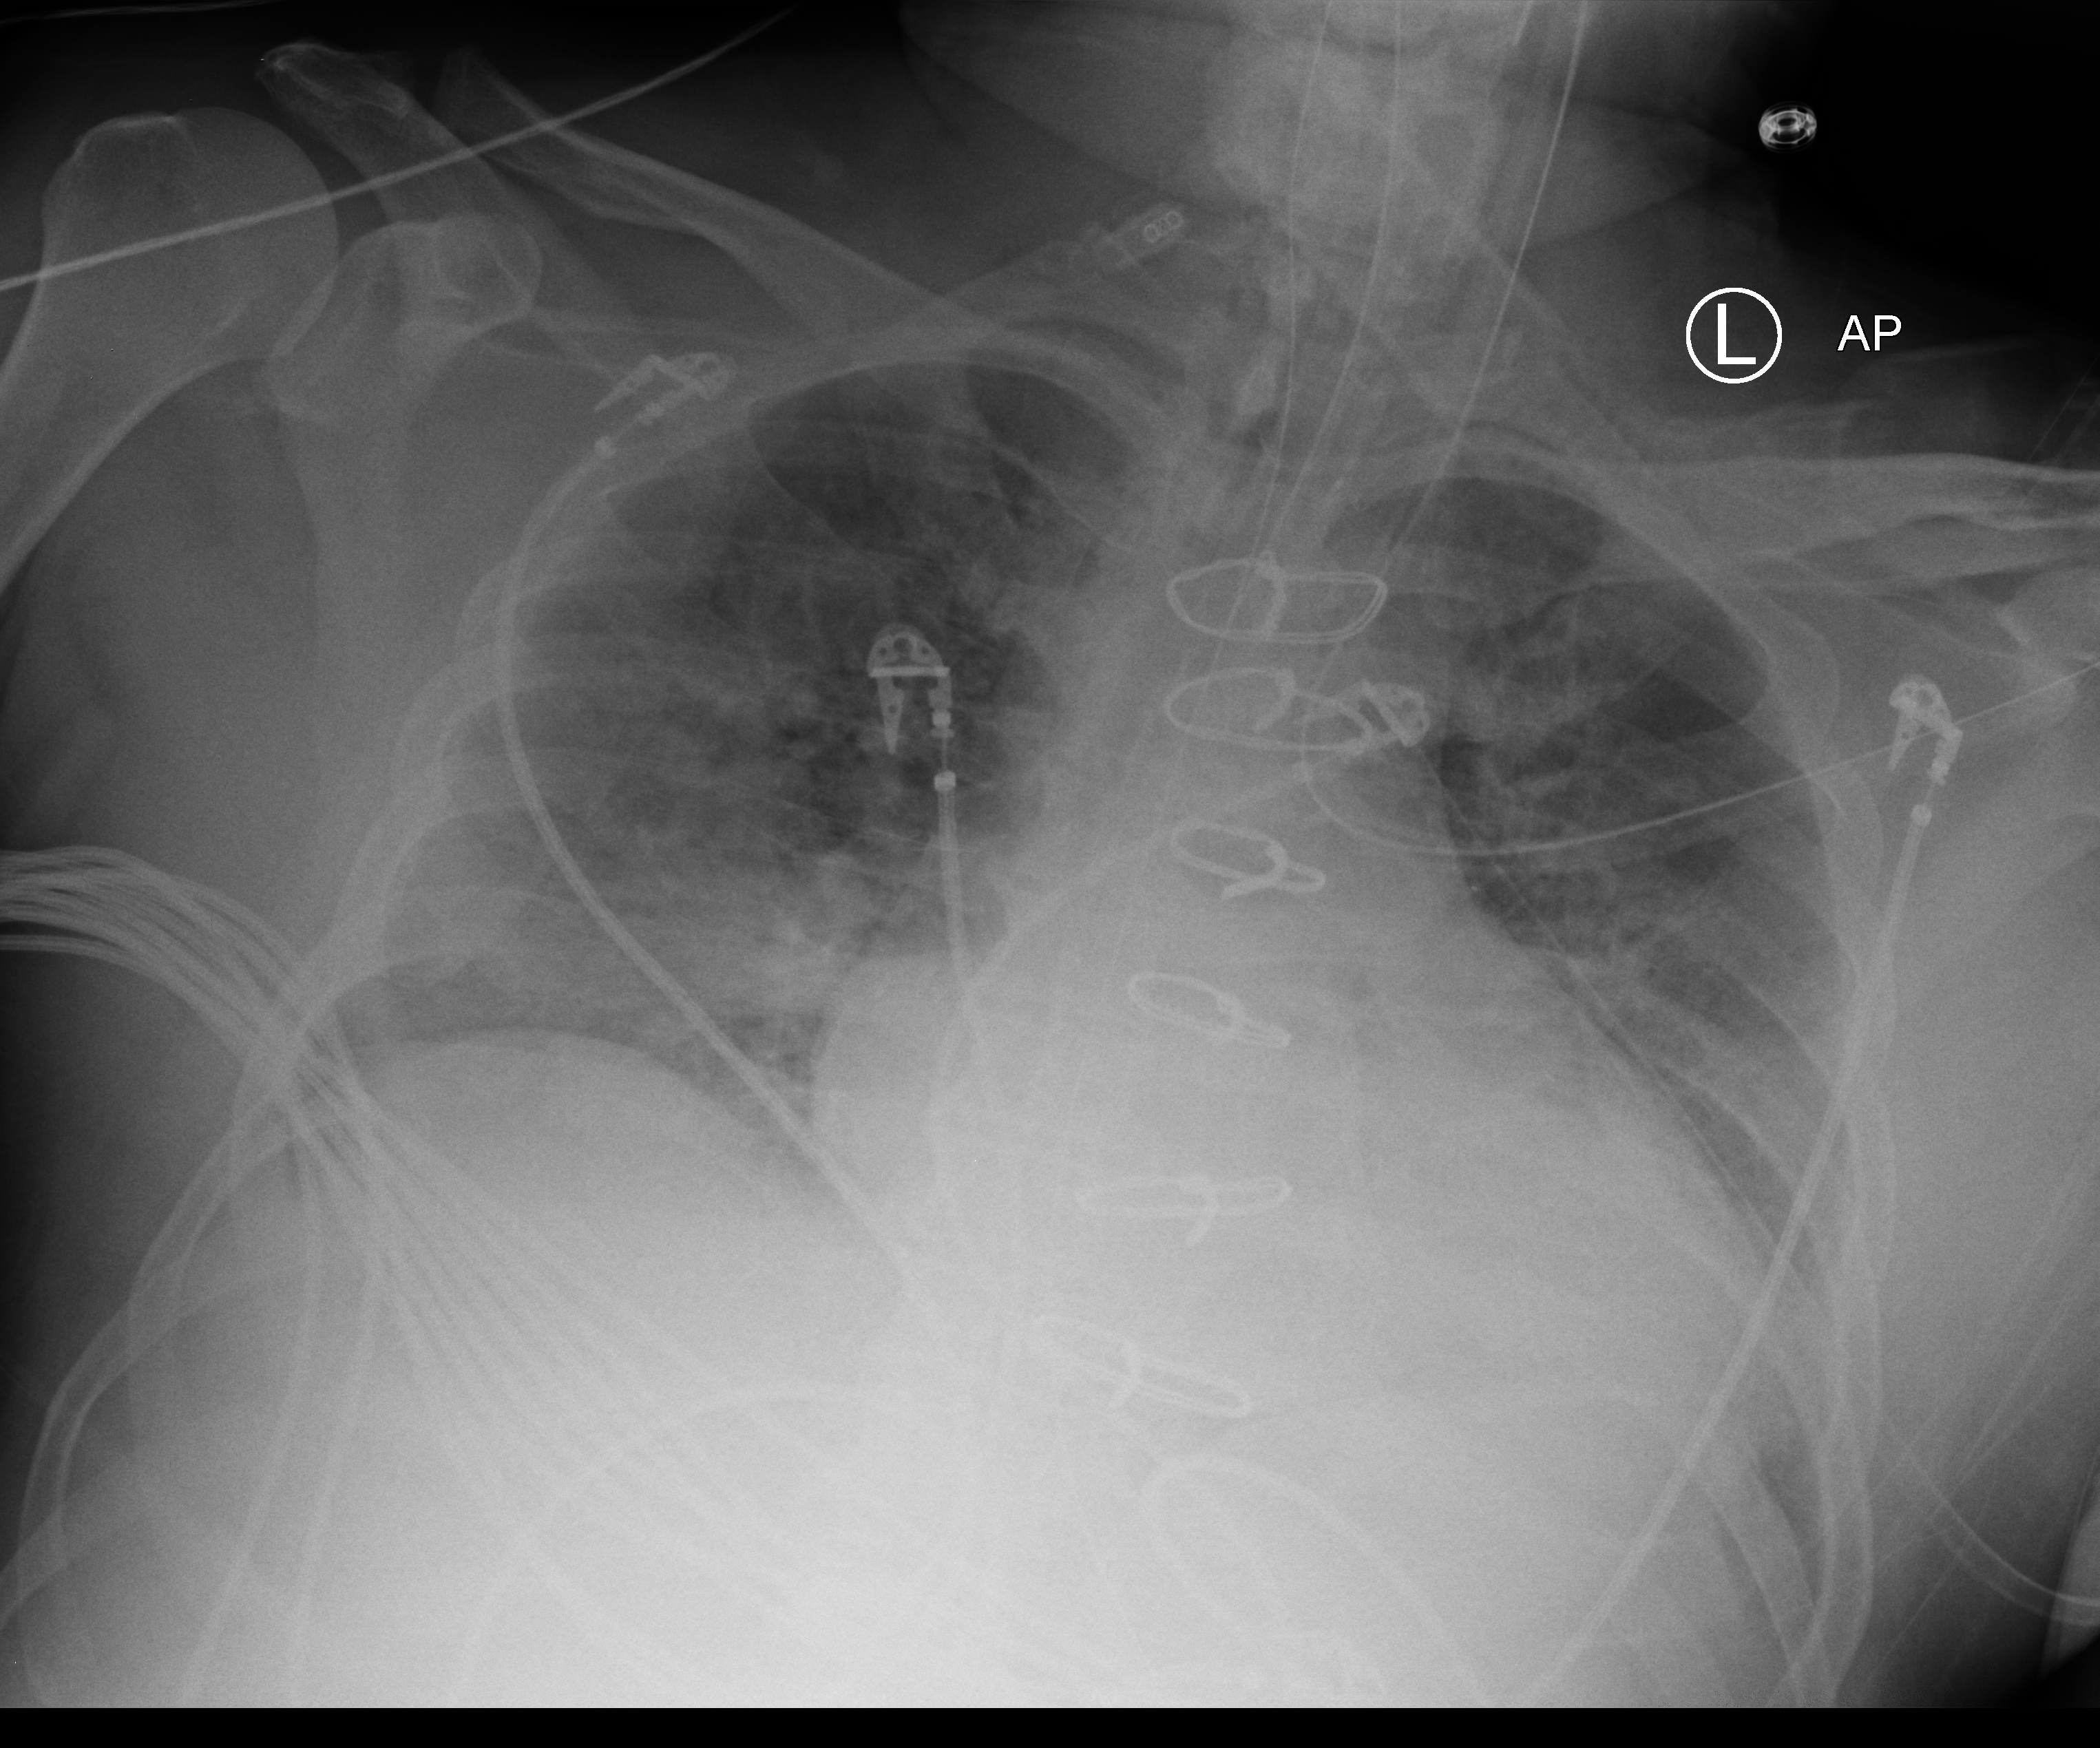
Chest X-ray (portable), anteroposterior (AP) projection. Patient hospitalised with COVID-19, aged 18–59 years.
Hospital-stay facts (about this admission, not read from this image; timing relative to this image not recorded): diabetes (admission record): yes.